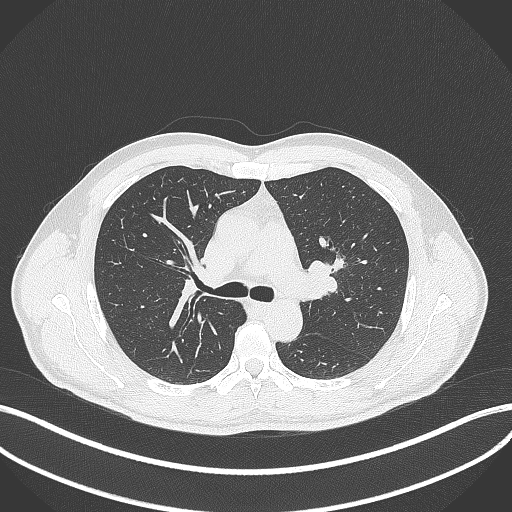
Chest CT, one axial slice; position 273 of 392 along the scan axis; reconstruction kernel B70f; 120 kVp; lung window (W 1500 / L -600 HU); 1 mm slice thickness; 512 × 512 image matrix. Patient: male, 50 years. From the clinical record (not read from this slice): clinical TNM (as recorded): T1c N1 M1b.
Outlined on this slice (rectangle marked by the reading radiologist):
- lung tumour (recorded histology: squamous cell carcinoma): box from (x=330, y=252) to (x=344, y=276) px